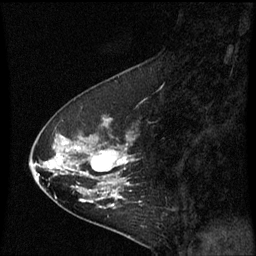
Breast MRI (dynamic contrast-enhanced), one sagittal slice. Slice 22 of 60 in the series (ordered by position). Dynamic contrast-enhanced series, image 2 of 3 at this slice position (ordered by acquisition). 1.5 T. TE 4.2 ms, TR 8.9 ms. 2 mm slice thickness. 256 × 256 image matrix, field of view 200 × 200 mm. Female patient, age 53 years. From the clinical record (not read from this slice): setting: breast cancer imaged before/during neoadjuvant chemotherapy; receptor status: HR-positive, HER2-negative.
Outlined on this slice (semi-automatic segmentation, software-assisted and operator-edited):
- analysis volume of interest (the breast-tissue region the enhancement analysis was run in; not a lesion): bounding box [x1, y1, x2, y2] px = [32, 104, 143, 221]
- tumour enhancement mask (voxels above the 70 % enhancement threshold inside the analysis volume of interest): [54, 120, 135, 197]